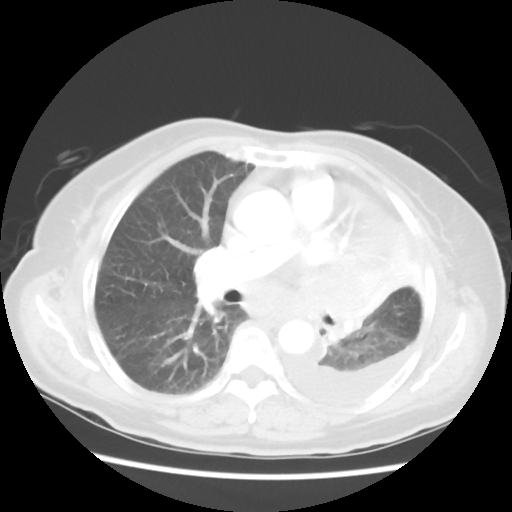
Chest CT, one axial slice; position 31 of 52 along the scan axis; lung window (W 1500 / L -600 HU); 5 mm slice thickness; 512 × 512 image matrix. Female patient, age 72 years. From the clinical record (not read from this slice): clinical TNM (as recorded): T4 N3 M1b; histopathological grade: G3.
Outlined on this slice (rectangle marked by the reading radiologist):
- lung tumour (recorded histology: large cell carcinoma): bounding box <299,262,374,355> (left, top, right, bottom; pixels)